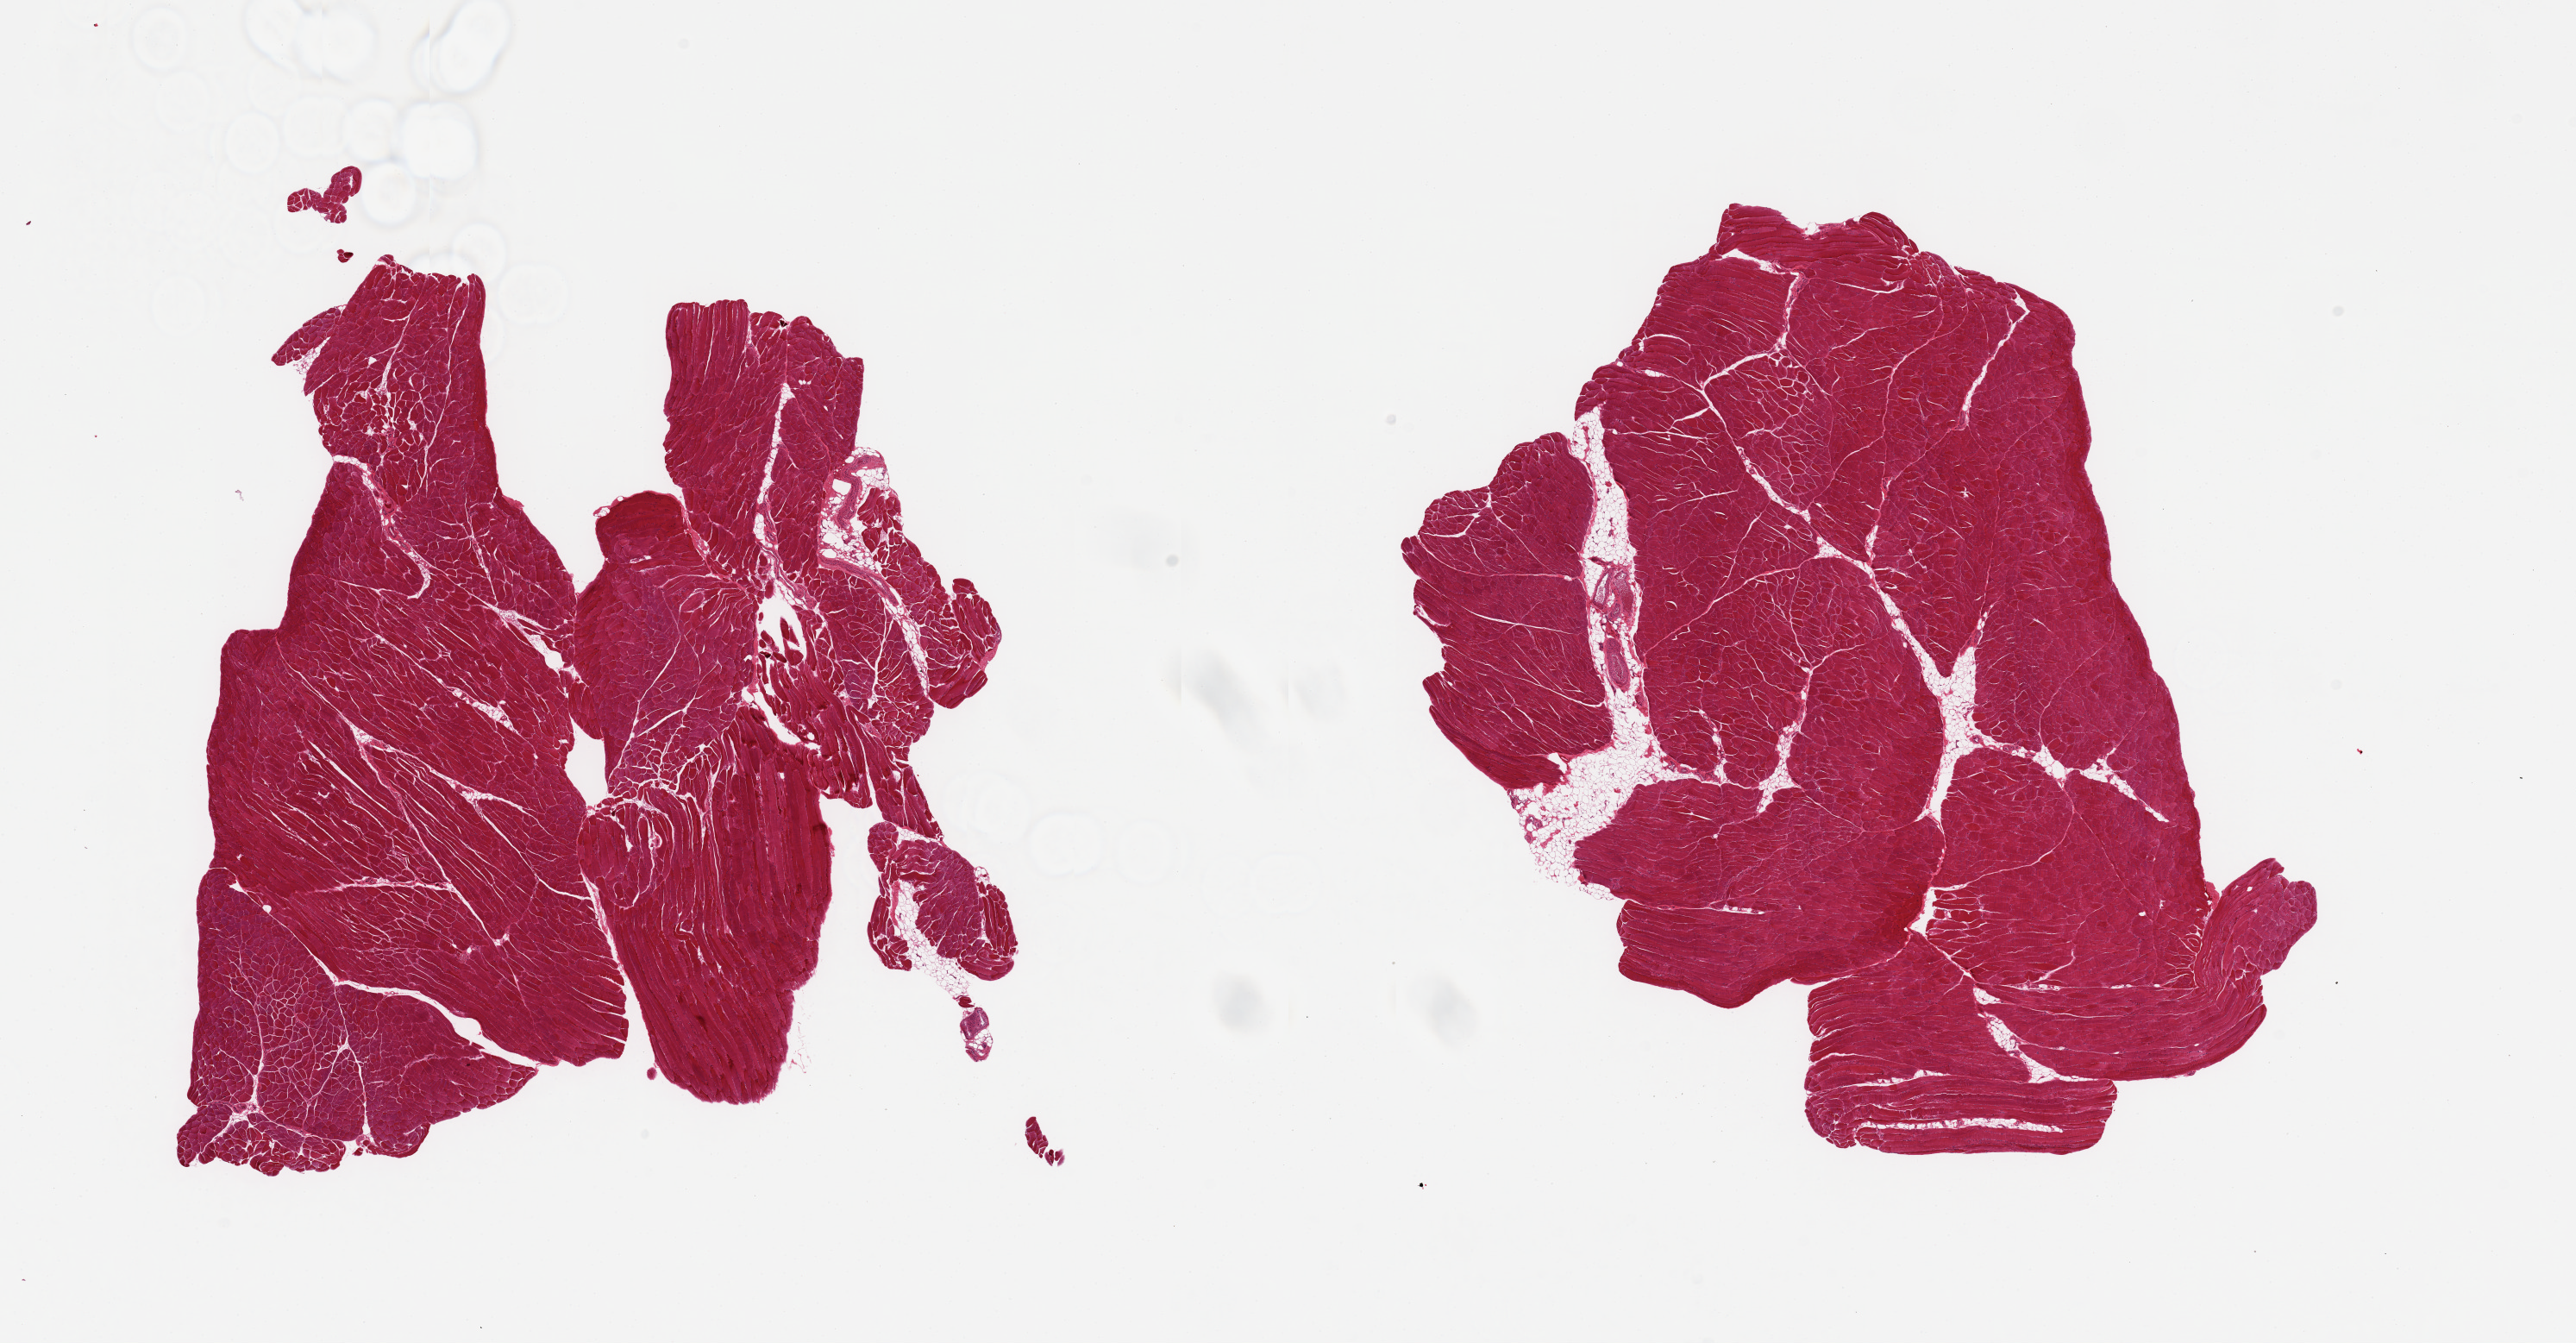
Digitized hematoxylin and eosin (H&E)-stained section — a low-resolution overview of the entire scanned area, about 23.6 x 12.3 mm (from a 20x scan). PAXgene-fixed, paraffin-embedded tissue. Target tissue: skeletal muscle. Donor tissue sample.
Pathologist's review note for this sample: 2 pieces; small amount of internal fat.